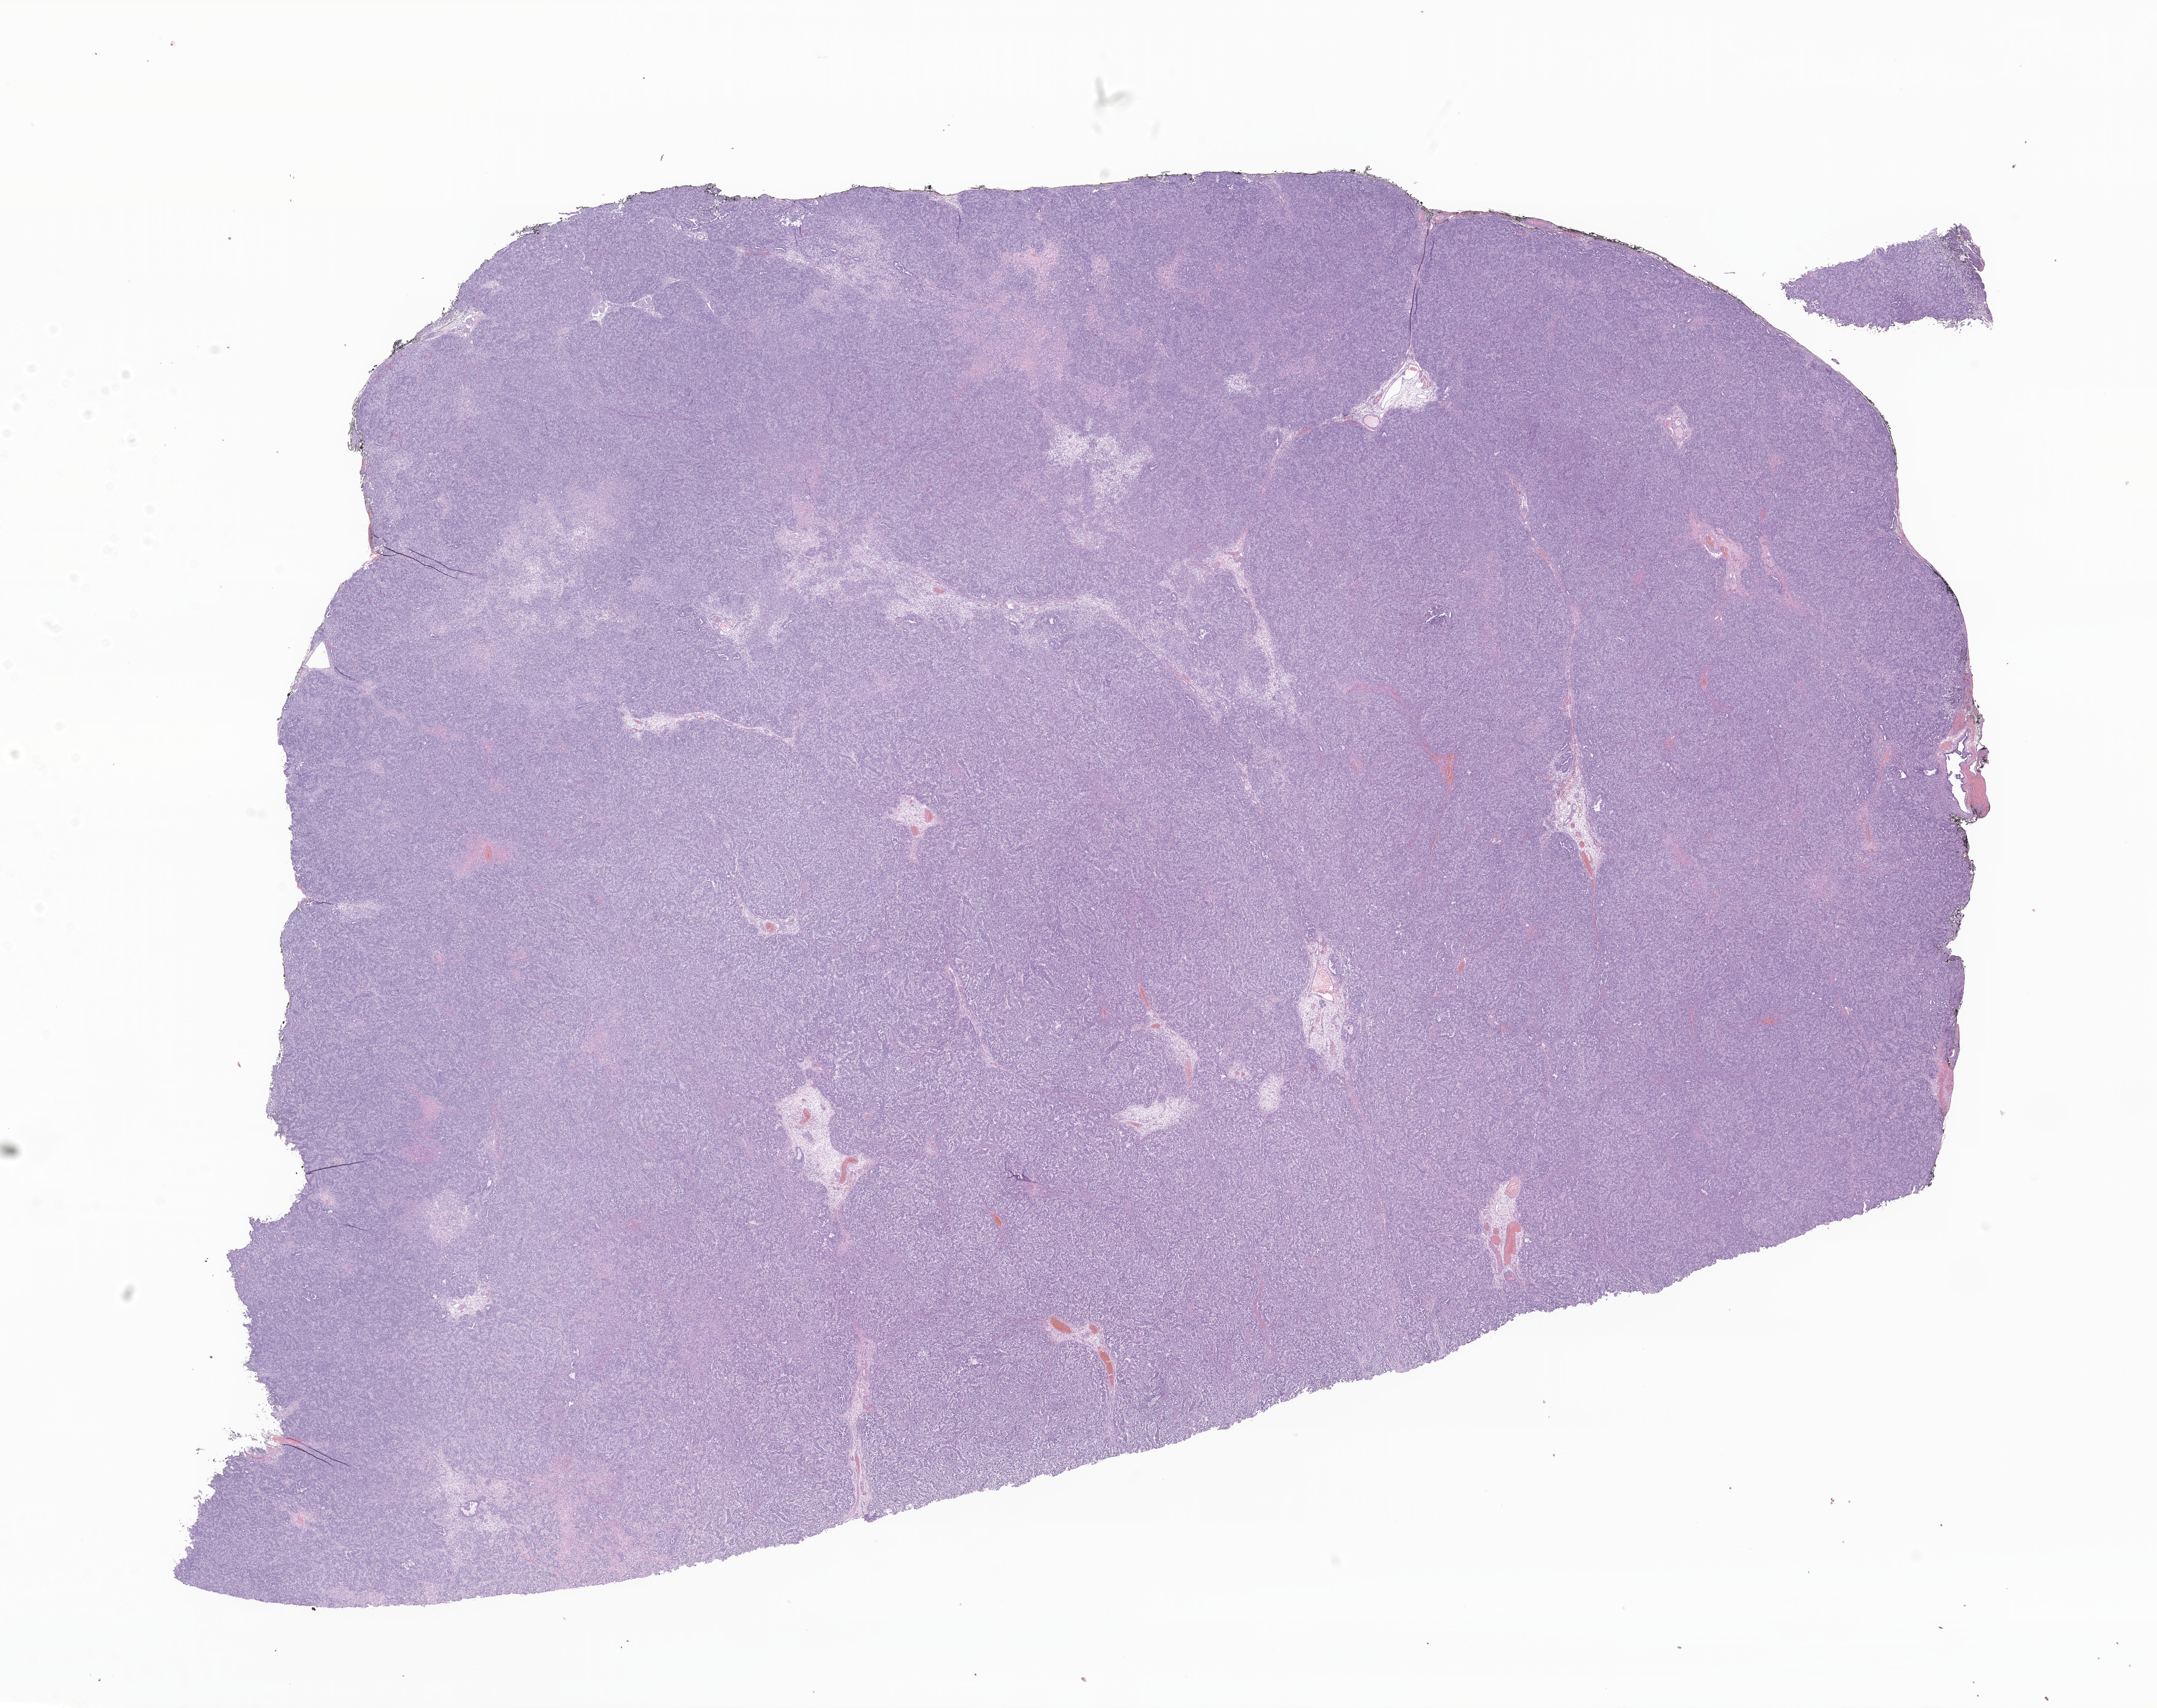
Digitized H&E-stained section of tumor tissue from the ovary — low-resolution overview of the scanned area, about 24.4 x 19.3 mm; FFPE section. Female patient, age 48 months (4 years).
- diagnosis (ICD-O-3 morphology term): Sertoli cell tumor, NOS